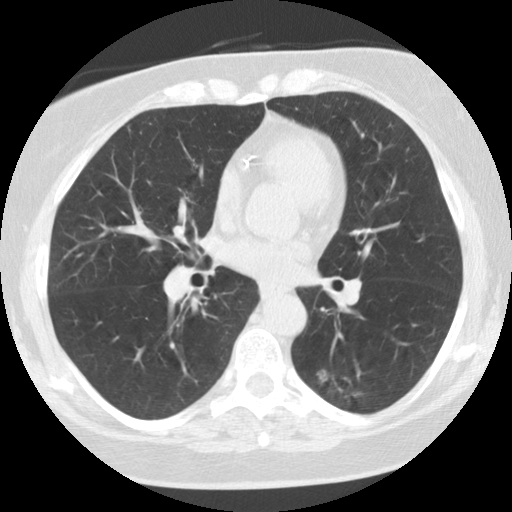
Axial slice from a low-dose chest CT screening exam; first (baseline) screen; lung window (W 1500 / L -600 HU); 2.5 mm slice thickness; standard (soft-tissue) reconstruction kernel (STANDARD); slice 62 of 115 in the series; 512 × 512 image matrix. Female, age 59 years at enrolment.
Expert reader's lesion annotation, box from (x=297, y=352) to (x=369, y=418) px. The screening reader recorded 5 non-calcified nodules or masses ≥4 mm on this exam; which of them this box marks is not recorded. Participant outcome: lung cancer diagnosed 707 days after this screen (after the third annual screen) — adenocarcinoma, NOS, left lower lobe, poorly differentiated (G3), stage IA (AJCC 6th edition), 15 mm at pathology.